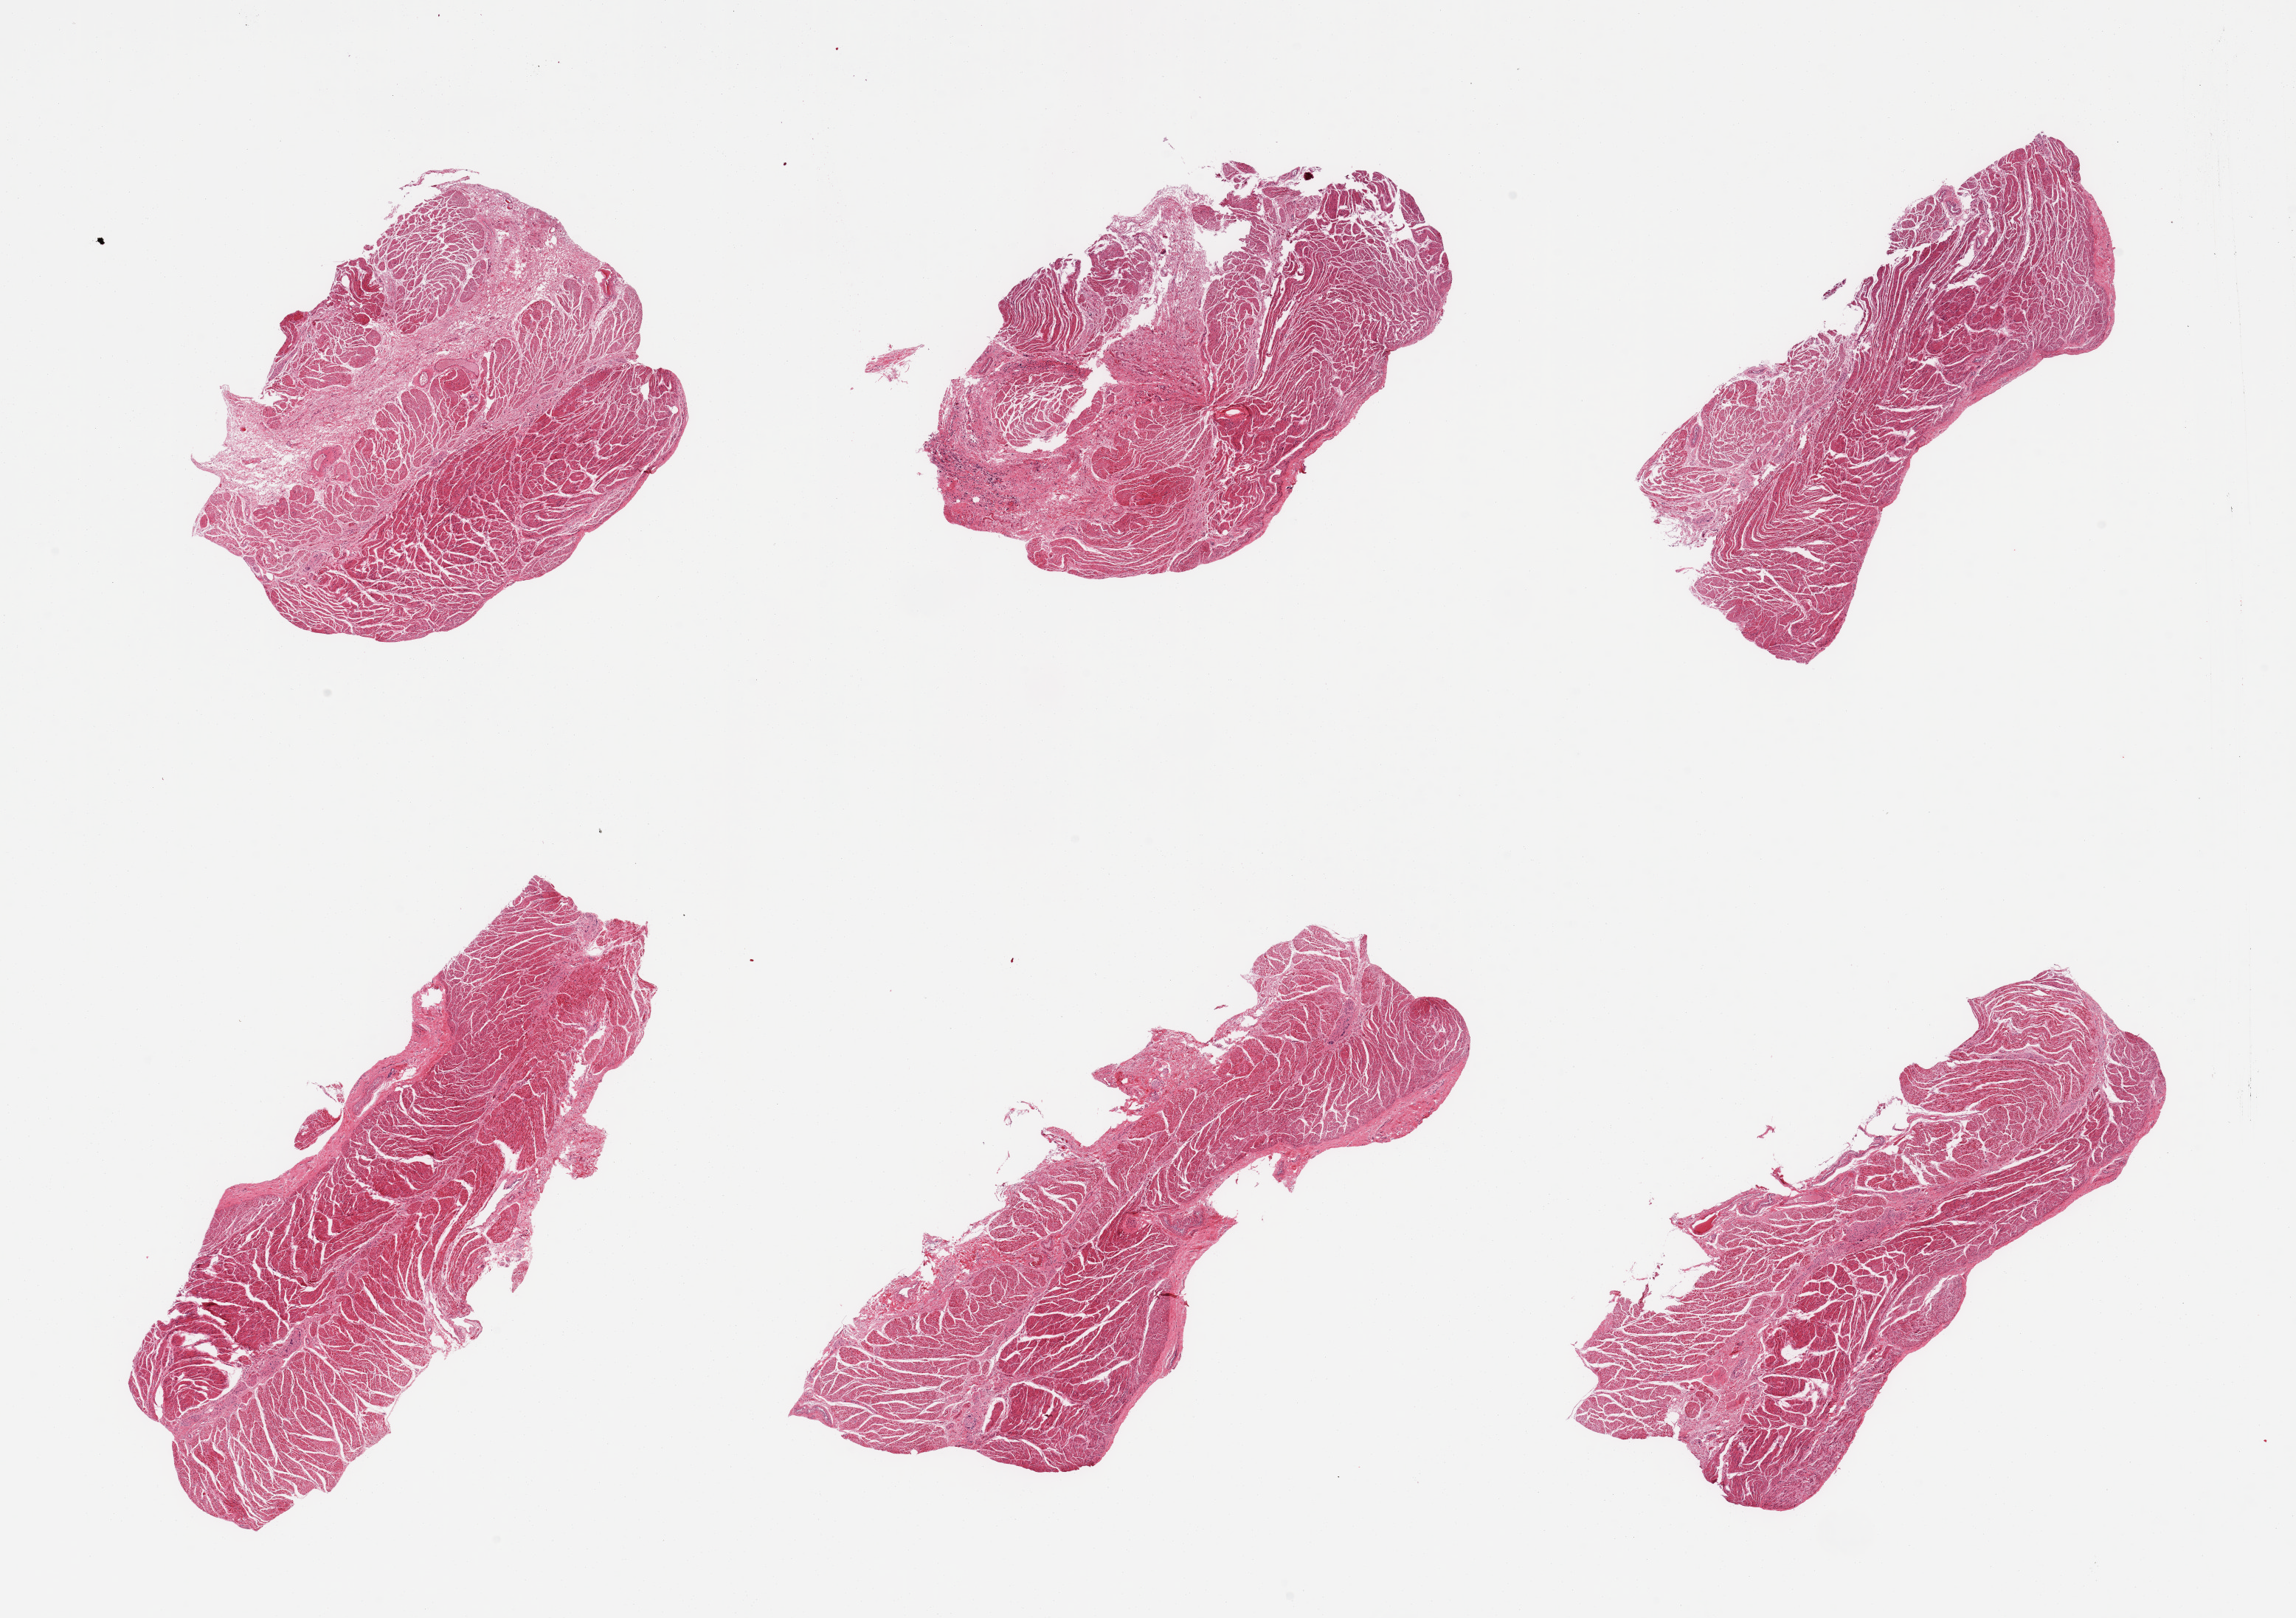
Whole-slide image, H&E stain, shown as a low-resolution overview of the whole scanned area (about 24.6 x 17.3 mm, slide scanned at 20x); PAXgene-fixed, paraffin-embedded tissue; section of gastroesophageal junction (target tissue); donor tissue sample. Donor: female.
Reviewer comment on this tissue sample: 6 pieces; well dissected muscle.